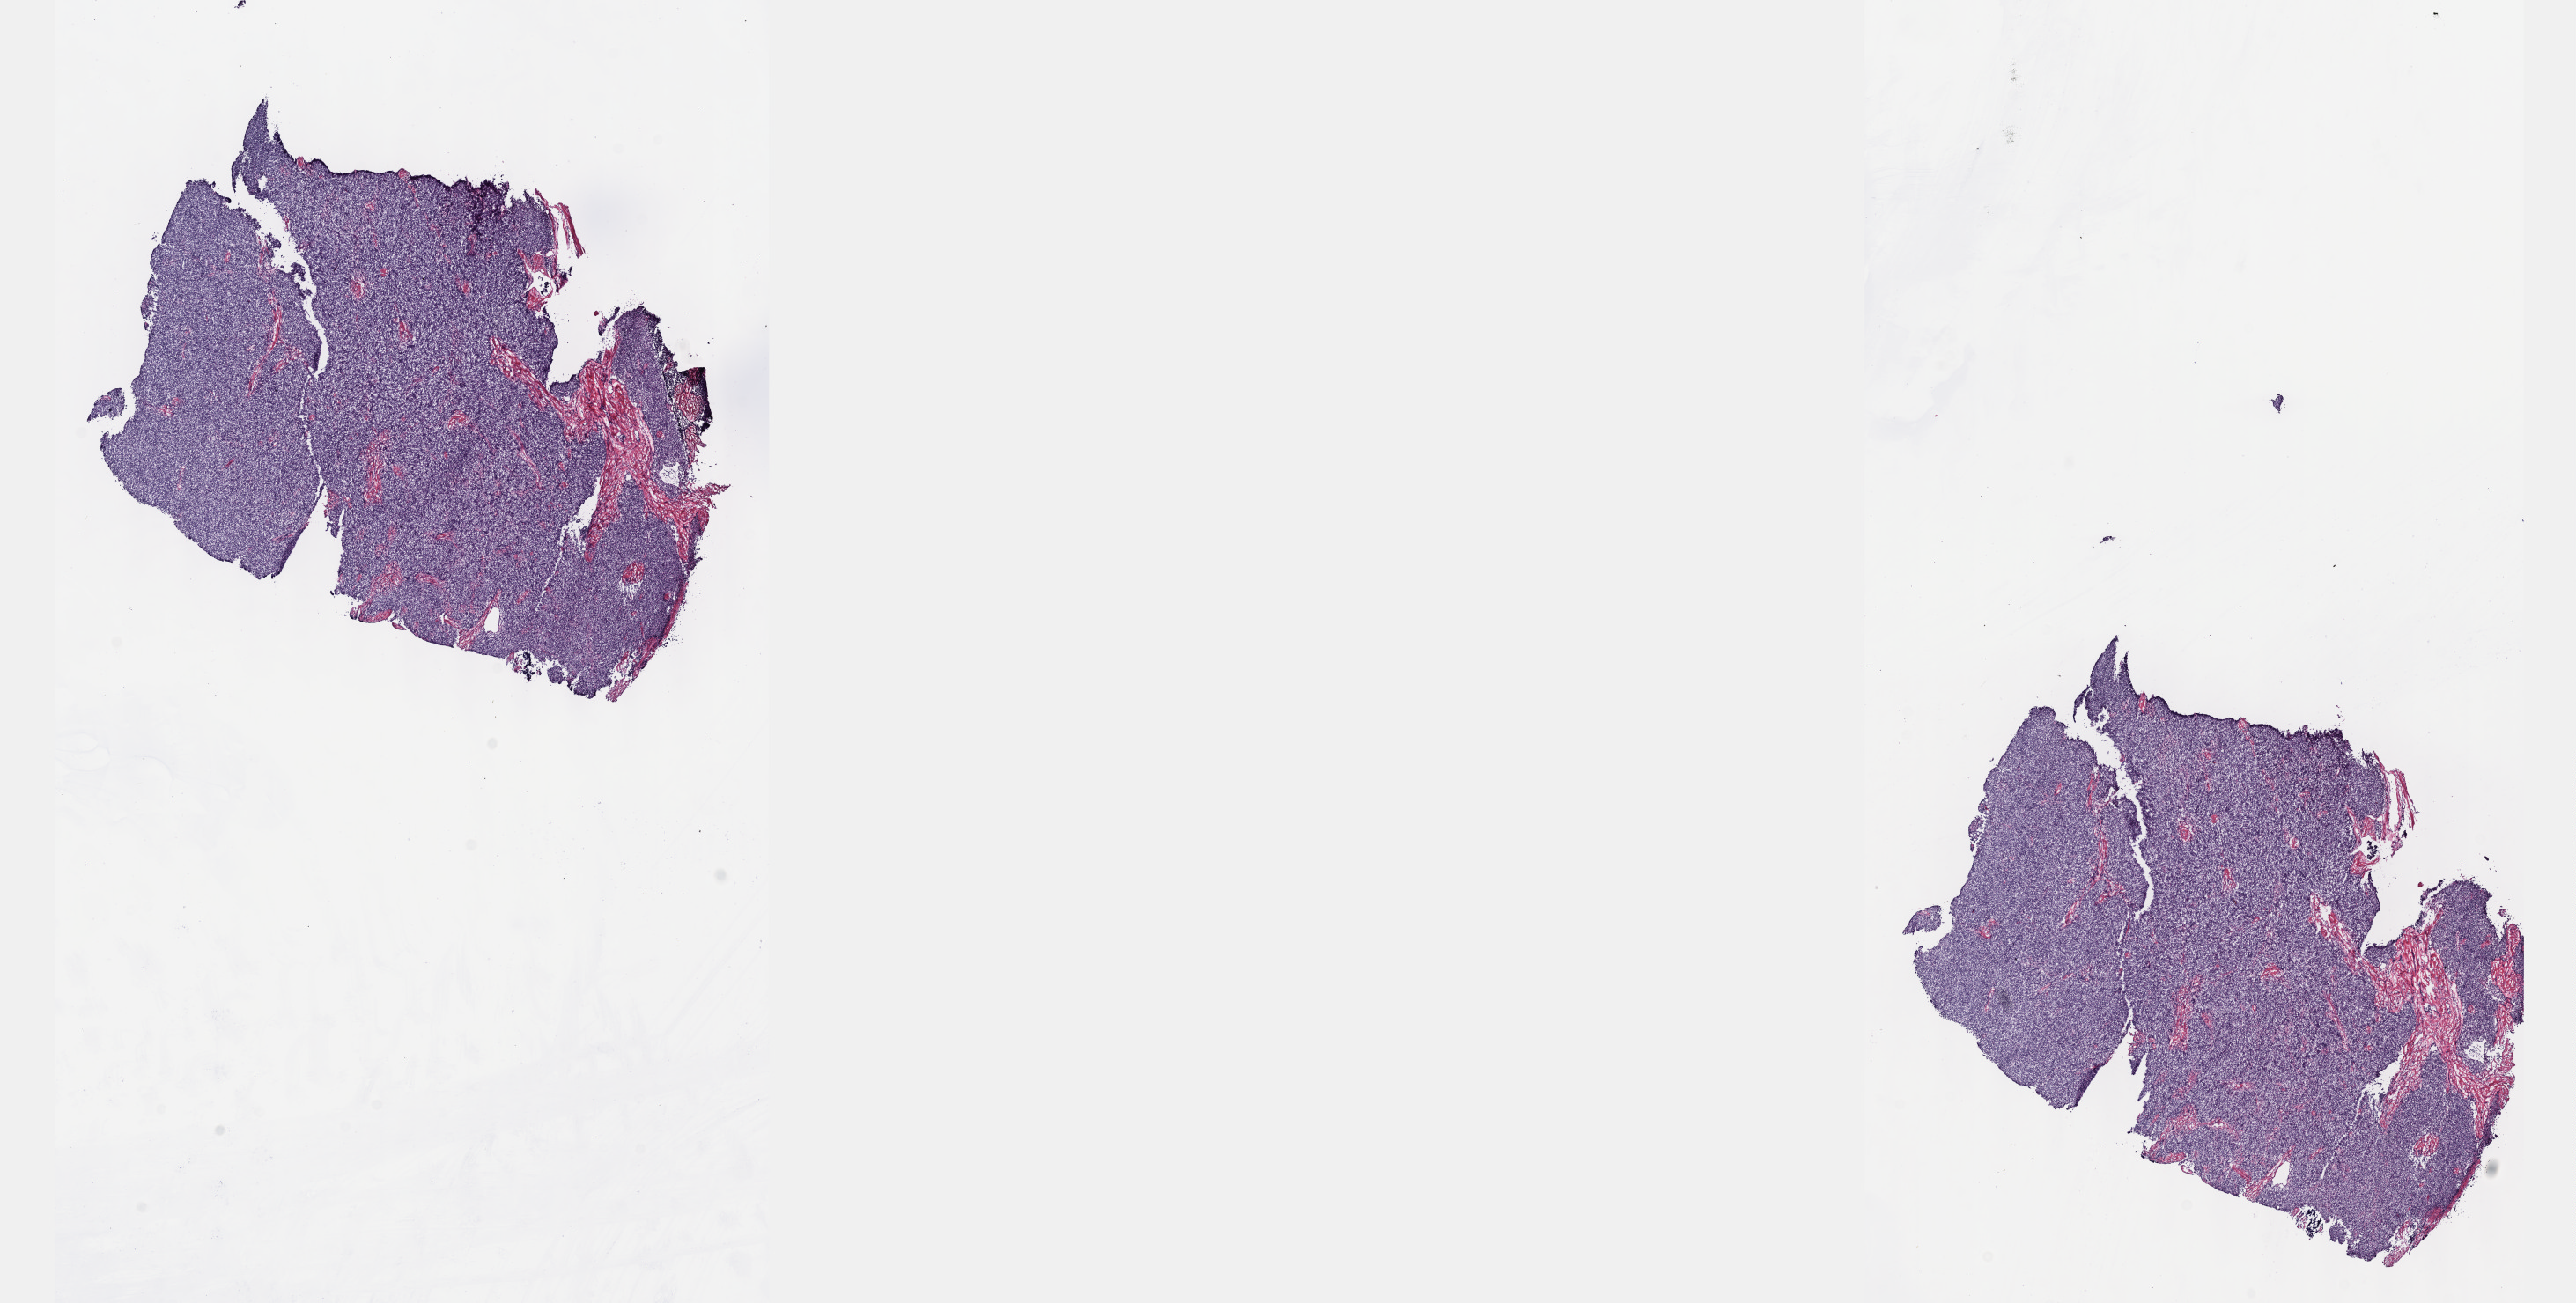
Digitized H&E-stained tissue section (whole slide) — shown as a low-resolution overview of the whole scanned area (about 23.6 x 12.0 mm); frozen section from the top of the tissue portion; sample: primary tumour, thymus. Male patient; age at initial diagnosis 51 years. Composition of this section per pathologist review: tumour cells 100%, tumour nuclei 80%, normal cells 0%, stromal cells 0%, necrosis 0%. Inflammatory infiltration, as recorded: lymphocyte infiltration 2%, monocyte infiltration 0%, neutrophil infiltration 0%.
Diagnosis: Thymoma, type AB, NOS (anterior mediastinum).